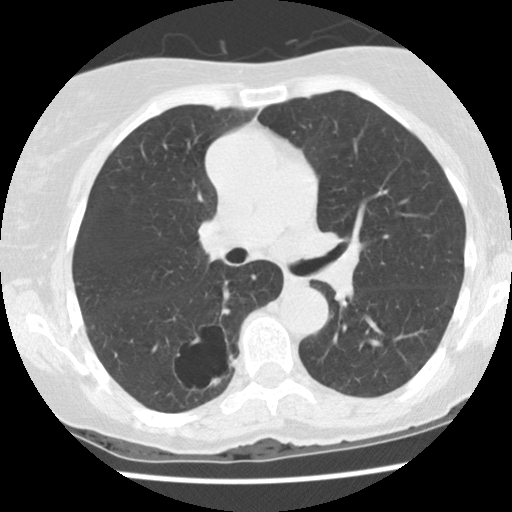
Low-dose screening chest CT, one axial slice; lung window (W 1500 / L -600 HU); 512 × 512 image matrix, field of view 300 × 300 mm.
Structures marked on this image (outlined manually by an expert reader):
- lesion 1 (tumor, lower lobe of right lung): box from (x=210, y=358) to (x=235, y=385) px